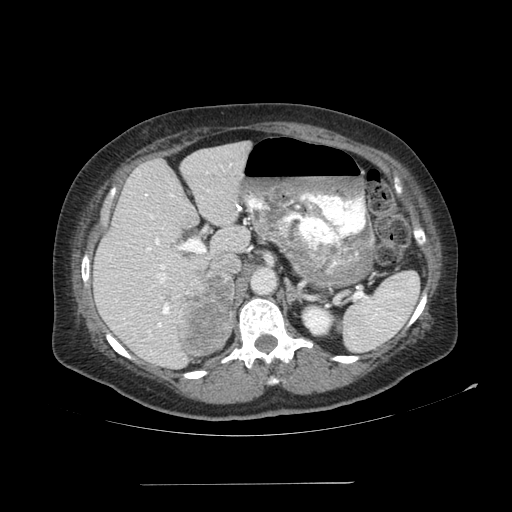
Contrast-enhanced abdominal CT, one axial slice. Slice 67 of 113 in the series (ordered by position). Reconstruction kernel SOFT. 120 kVp. Soft-tissue window (W 400 / L 40 HU). 512 × 512 image matrix, field of view 440 × 440 mm. Female patient, age 67 years. Case-level facts recorded for this patient, not image findings: diagnosis: adrenocortical carcinoma; tumour side: right adrenal; tumour size at pathology: 9.8 cm; Ki-67 index: 59 %; stage (as recorded): 4.
Structures marked on this image (semi-automatic segmentation, software-assisted and operator-edited):
- mass: bounding box [x1, y1, x2, y2] px = [178, 271, 232, 355]